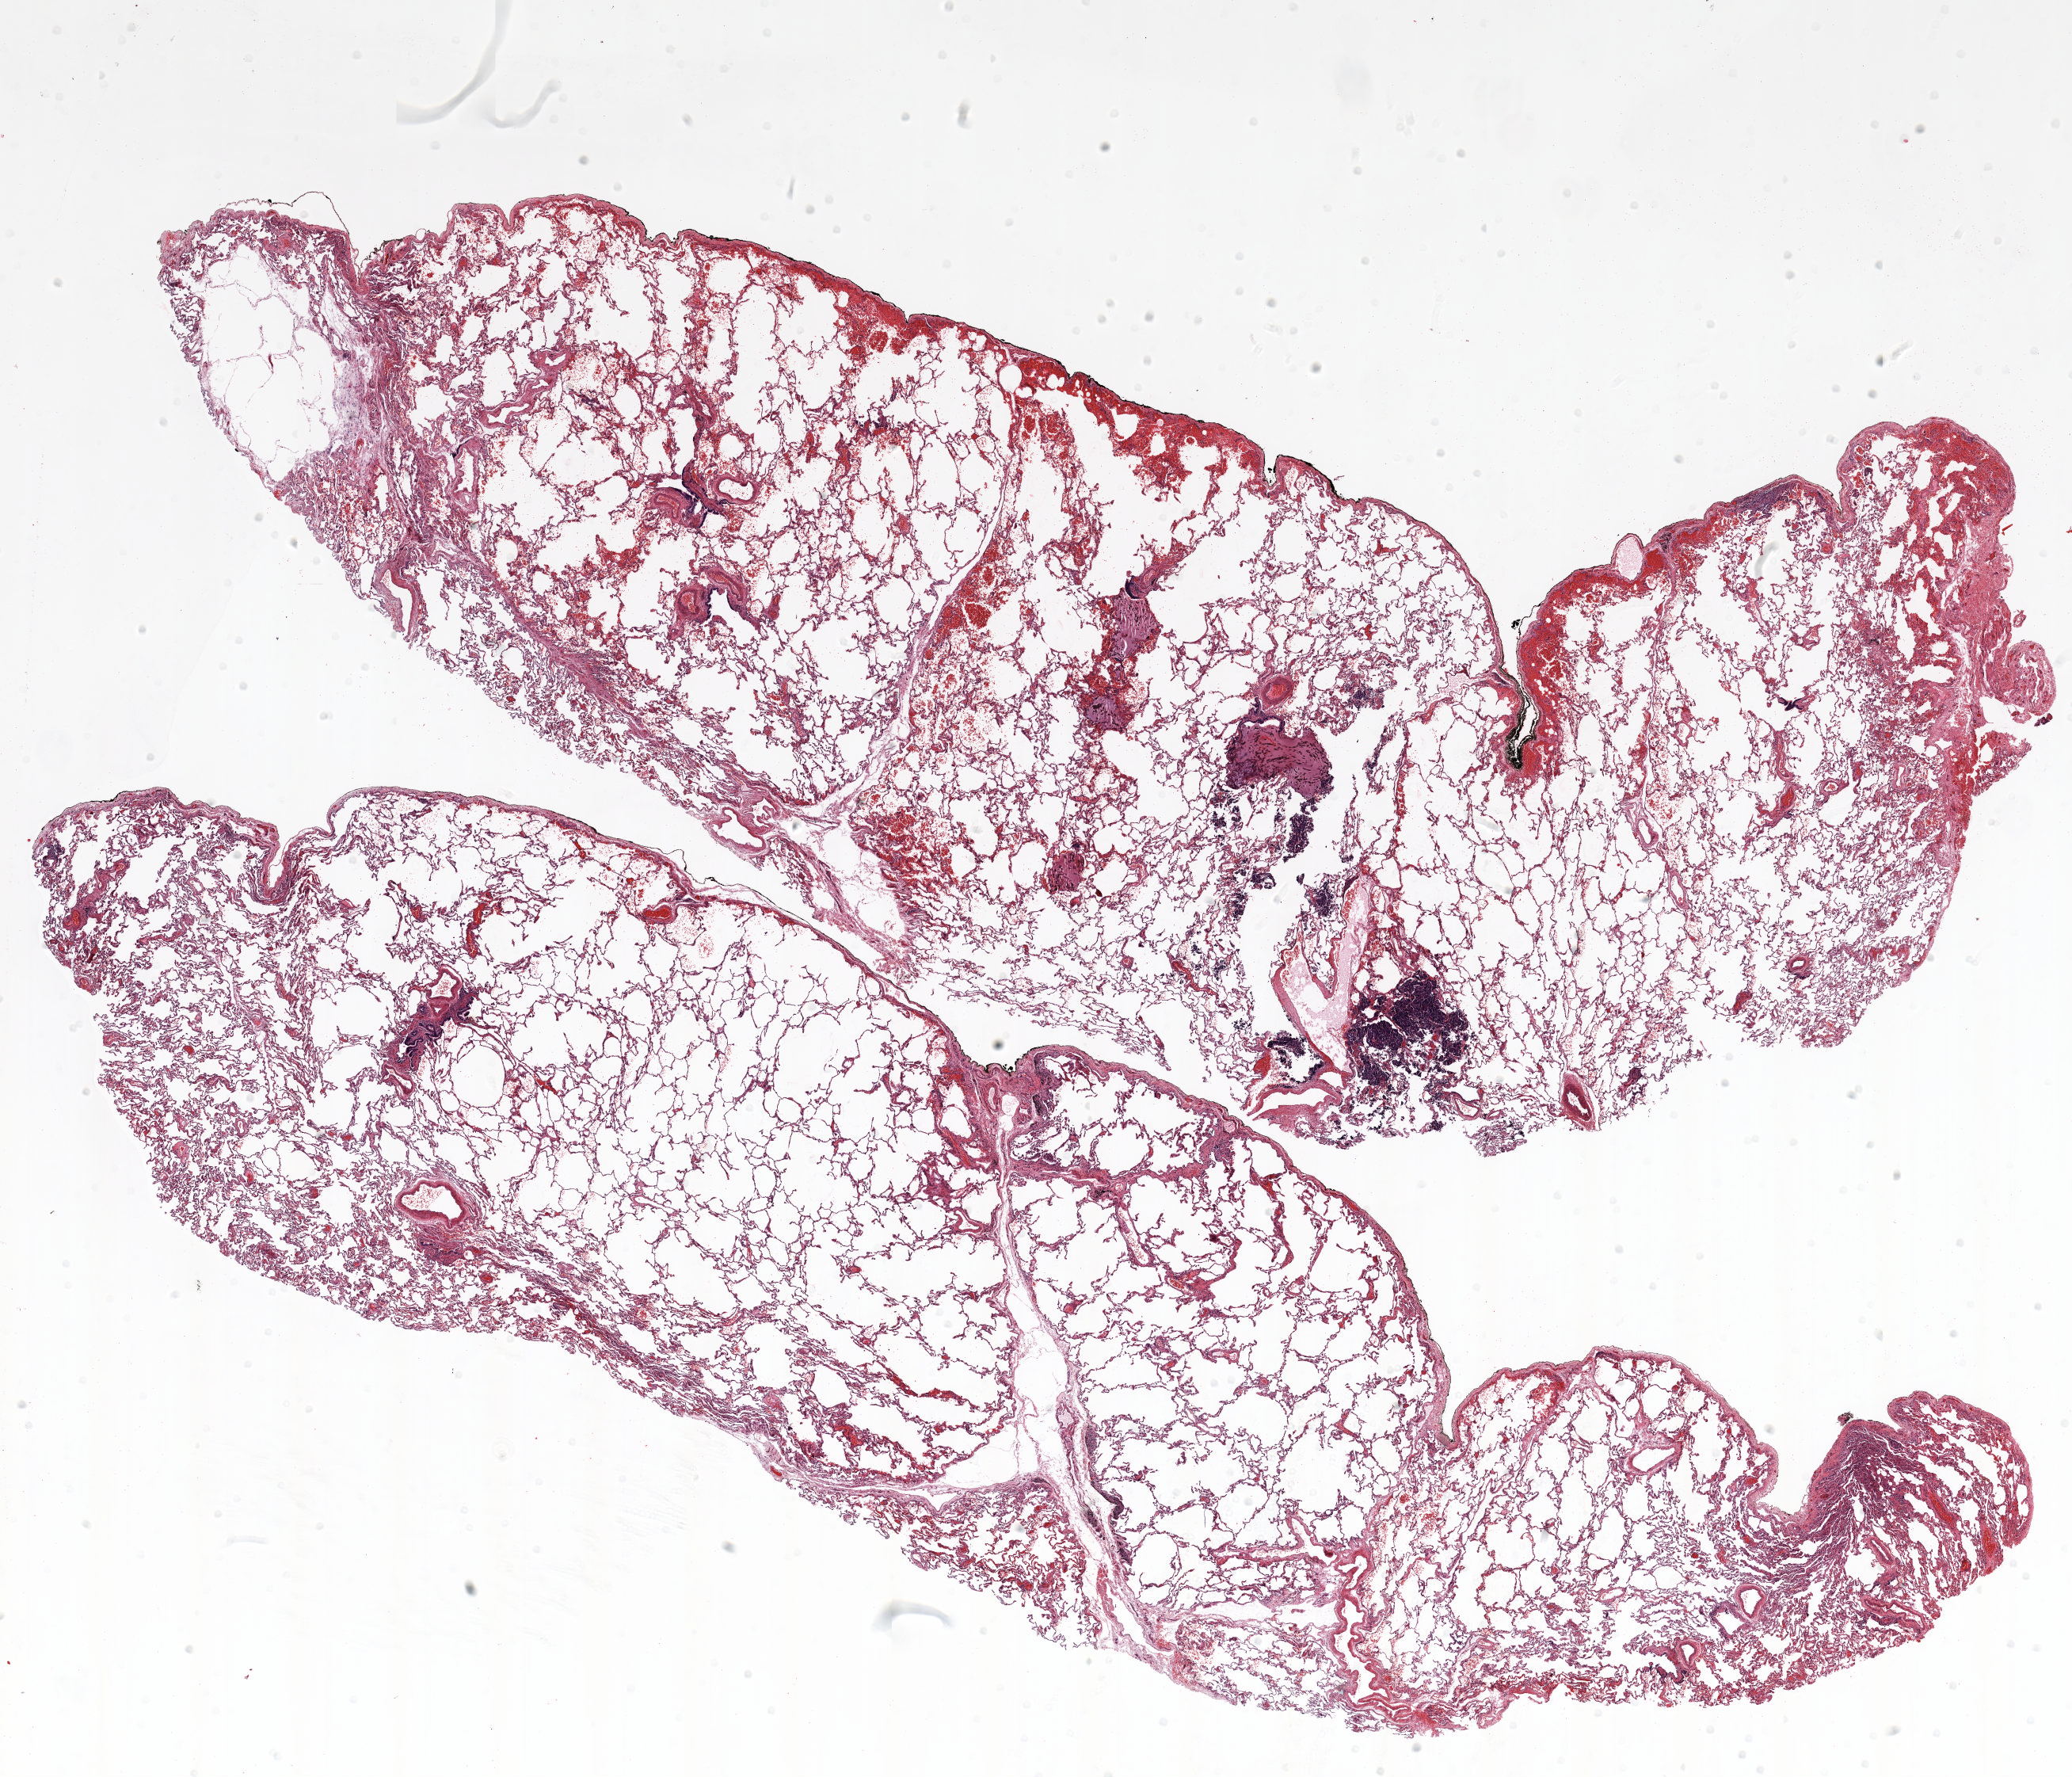
Whole-slide histology image, H&E-stained — shown as a low-resolution overview of the whole scanned area (about 21.0 x 18.0 mm), FFPE section, lung tissue. Female patient, aged 60 at enrolment. Former smoker at enrolment.
• stage (AJCC 6th edition): carcinoid, stage not assessed
• primary tumour location (clinical record): left lower lobe
• participant's lung-cancer diagnosis: Carcinoid tumor, NOS
• tumour size (pathology): 13 mm
• ICD-O-3 topography: lower lobe of lung (C34.3)